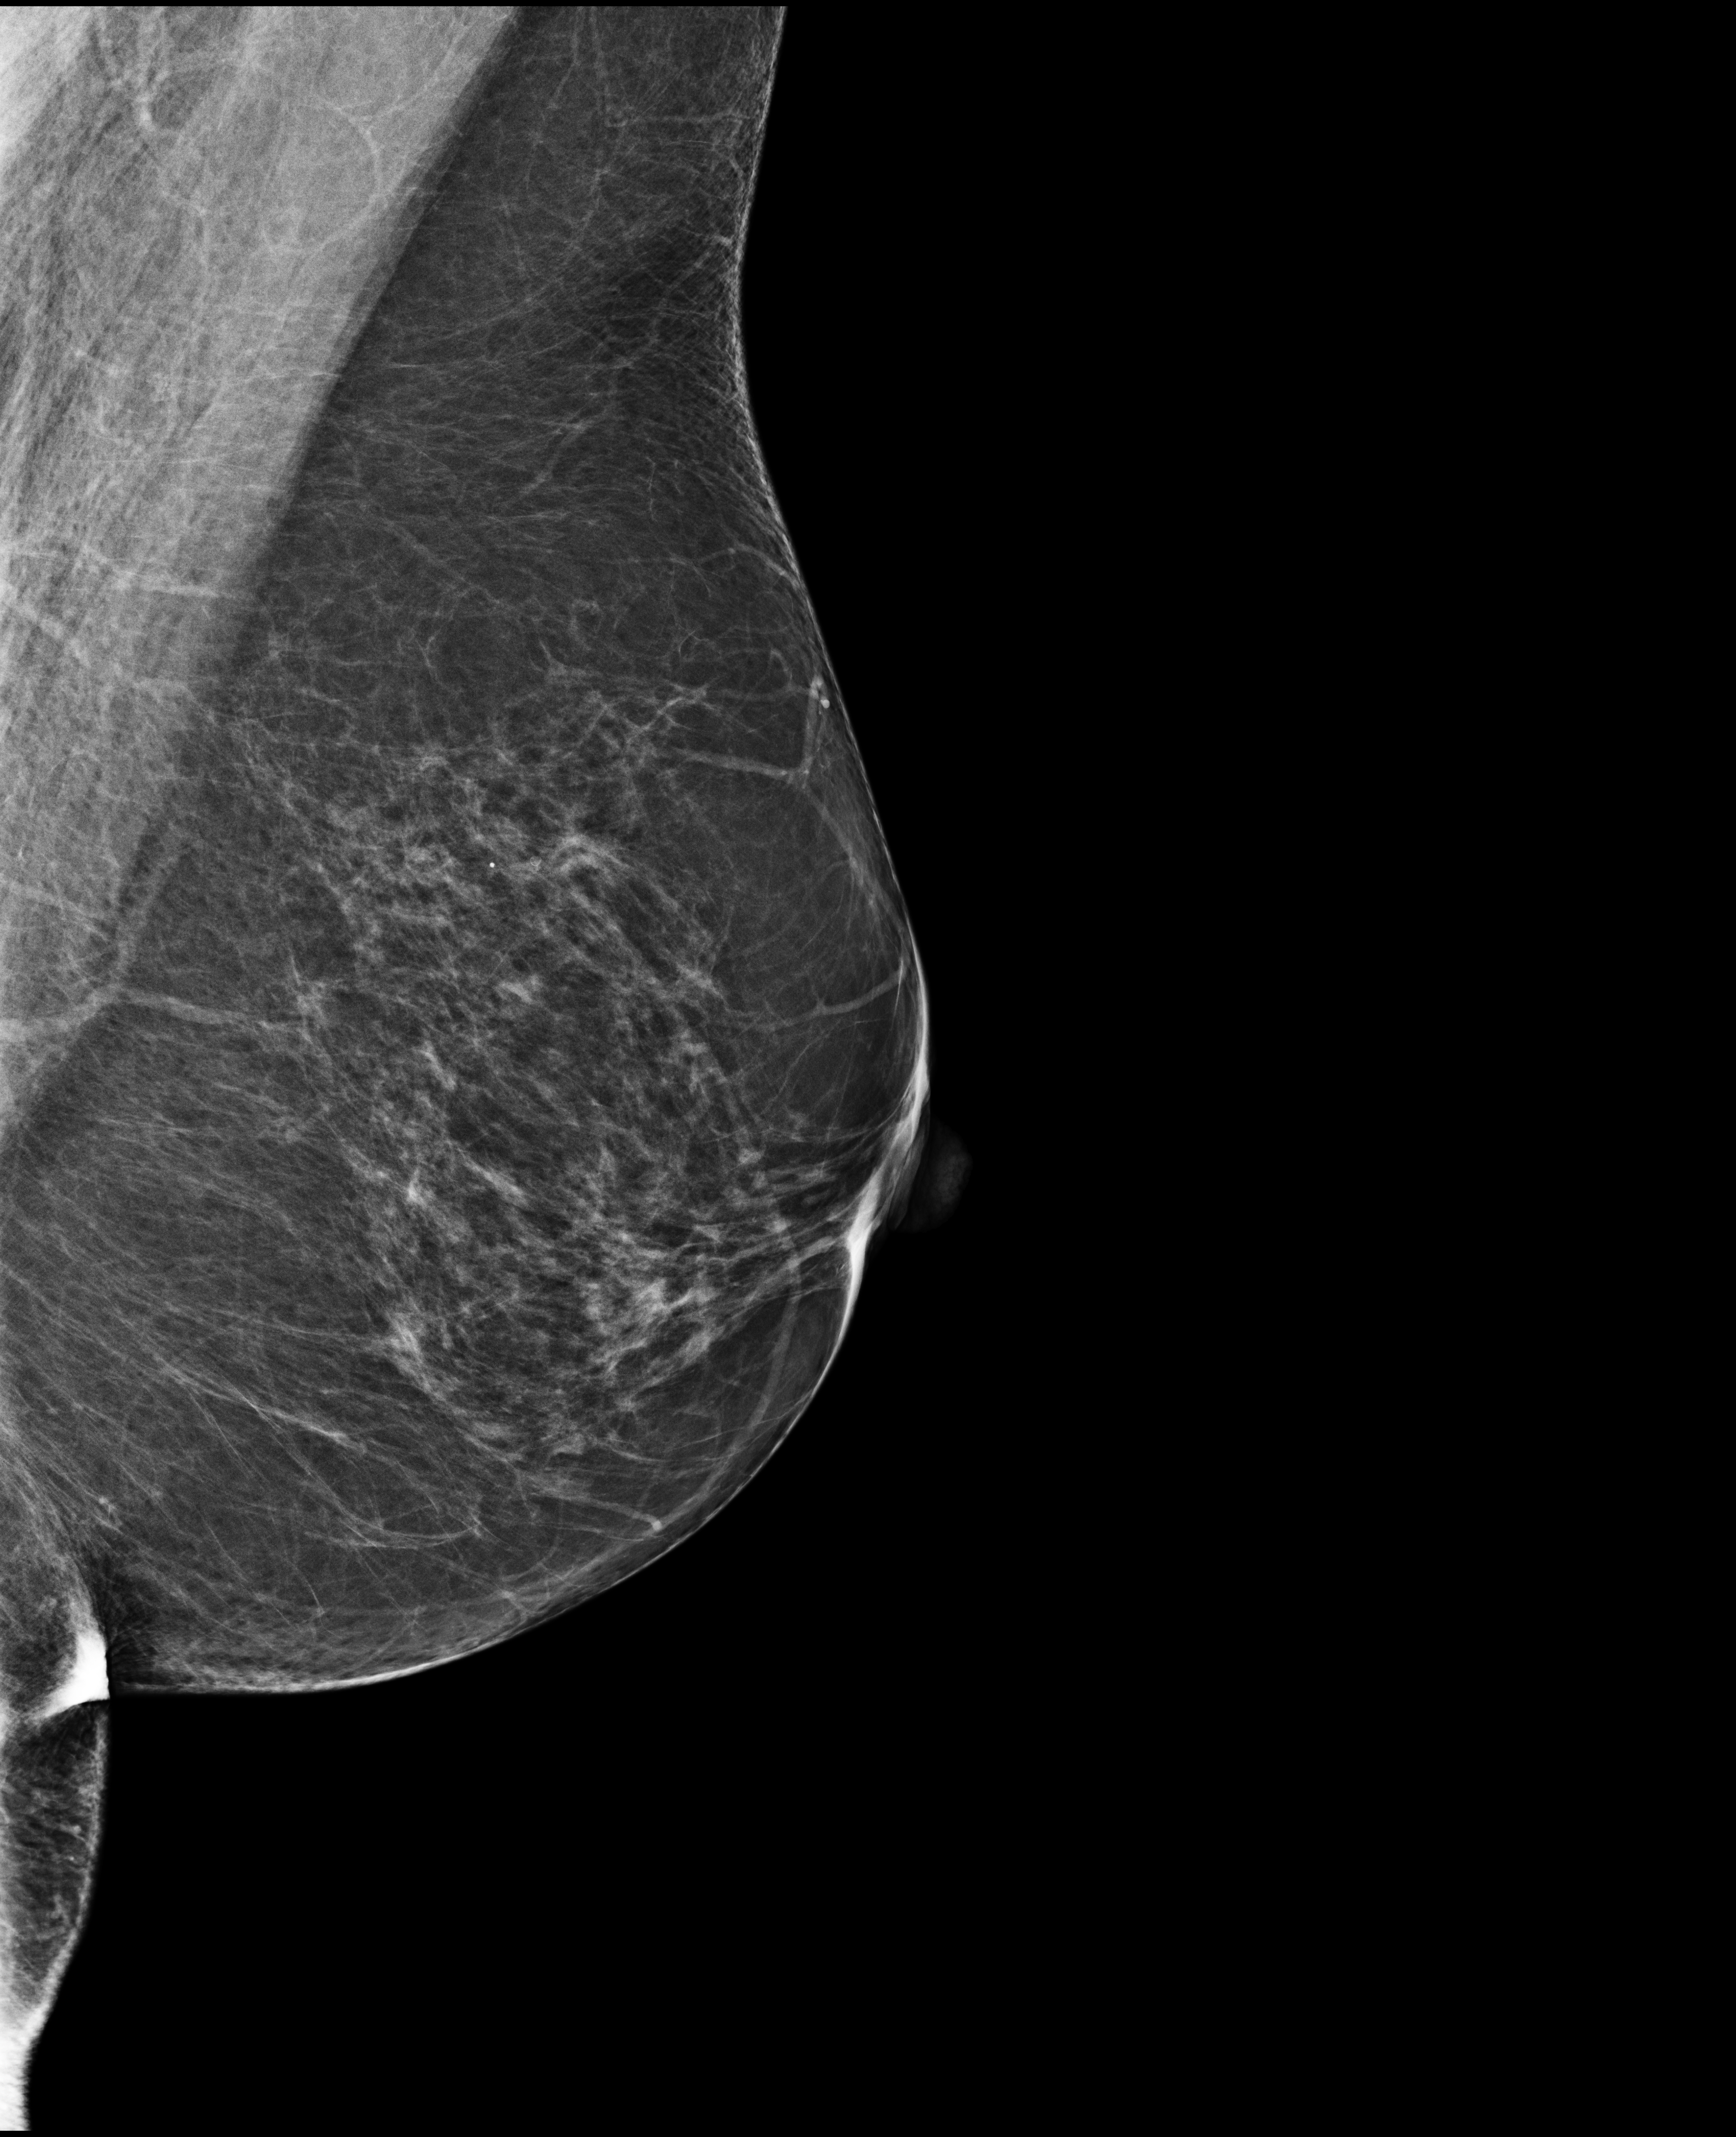
Full-field digital mammogram (FFDM), left breast, medio-lateral oblique projection, annual screening mammography examination. Patient: female, 74 years.
- breast density at the screening exam (both breasts): heterogeneously dense (BI-RADS density category c)
- final BI-RADS assessment for this screening round (tomosynthesis exam, both breasts): category 4
- recall: recalled for additional imaging after this screen